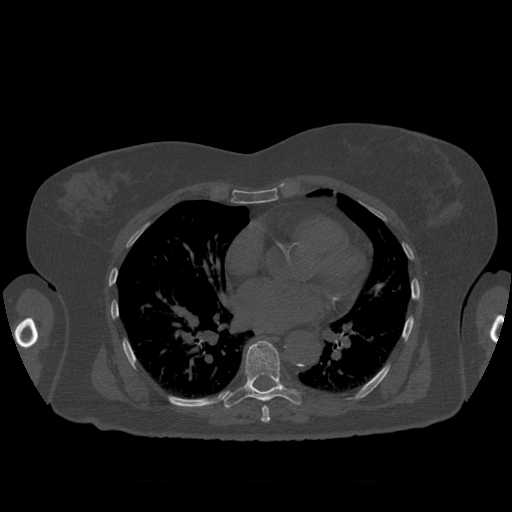
CT including the spine, one axial slice; slice 380 of 399 in the series (ordered by position); 120 kVp; bone window (W 1800 / L 400 HU); 1.25 mm slice thickness; 512 × 512 image matrix, field of view 404 × 404 mm. Patient age 81 years. From the clinical record (not read from this slice): primary cancer: renal; vertebrae with lytic lesions (as recorded): L1.
Annotated regions visible in this slice (semi-automatic segmentation, software-assisted and operator-edited):
- T7 vertebra: bounding box (x1, y1, x2, y2) in pixels: (261, 405, 271, 423)
- T8 vertebra: (223, 341, 301, 409)